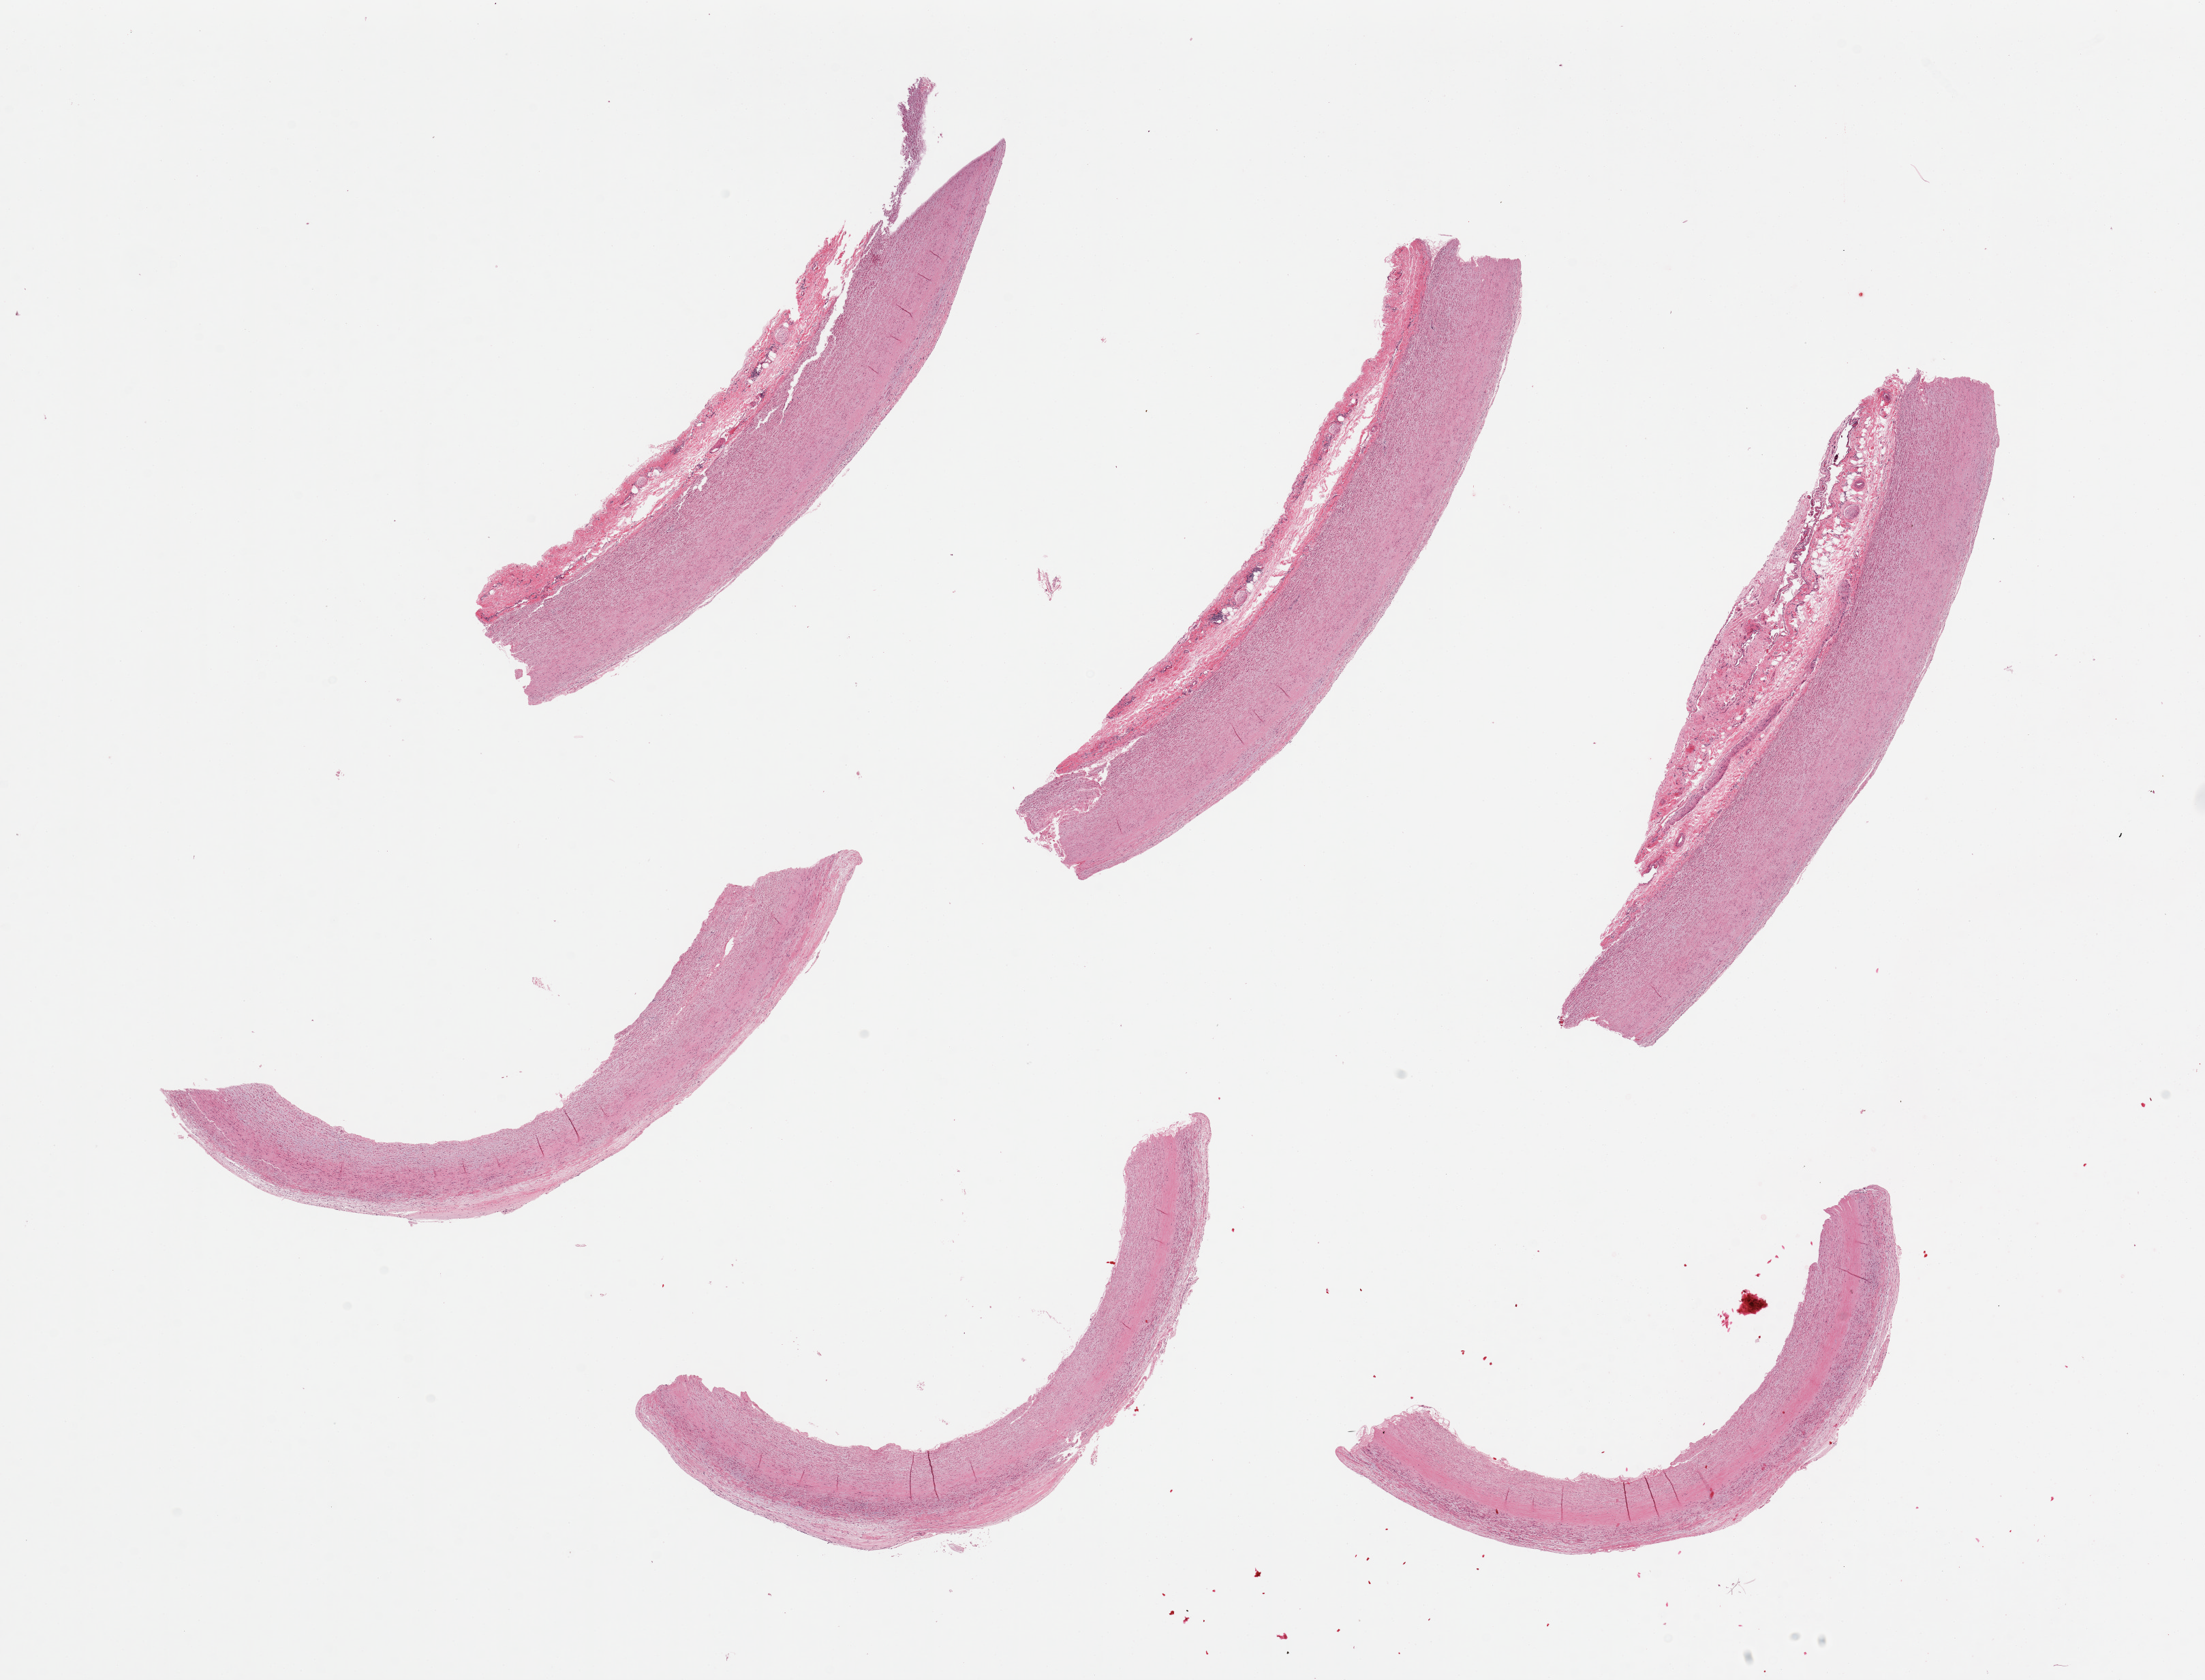
Whole-slide image, hematoxylin and eosin (H&E) stain, brightfield, low-resolution overview of the scanned area, about 25.6 x 19.5 mm (acquisition: 20x scan). PAXgene-fixed, paraffin-embedded tissue. Target tissue: aorta. Donor tissue sample. Female donor.
Reviewer comment on this tissue sample: 6 pieces, mild atherosclerosis.